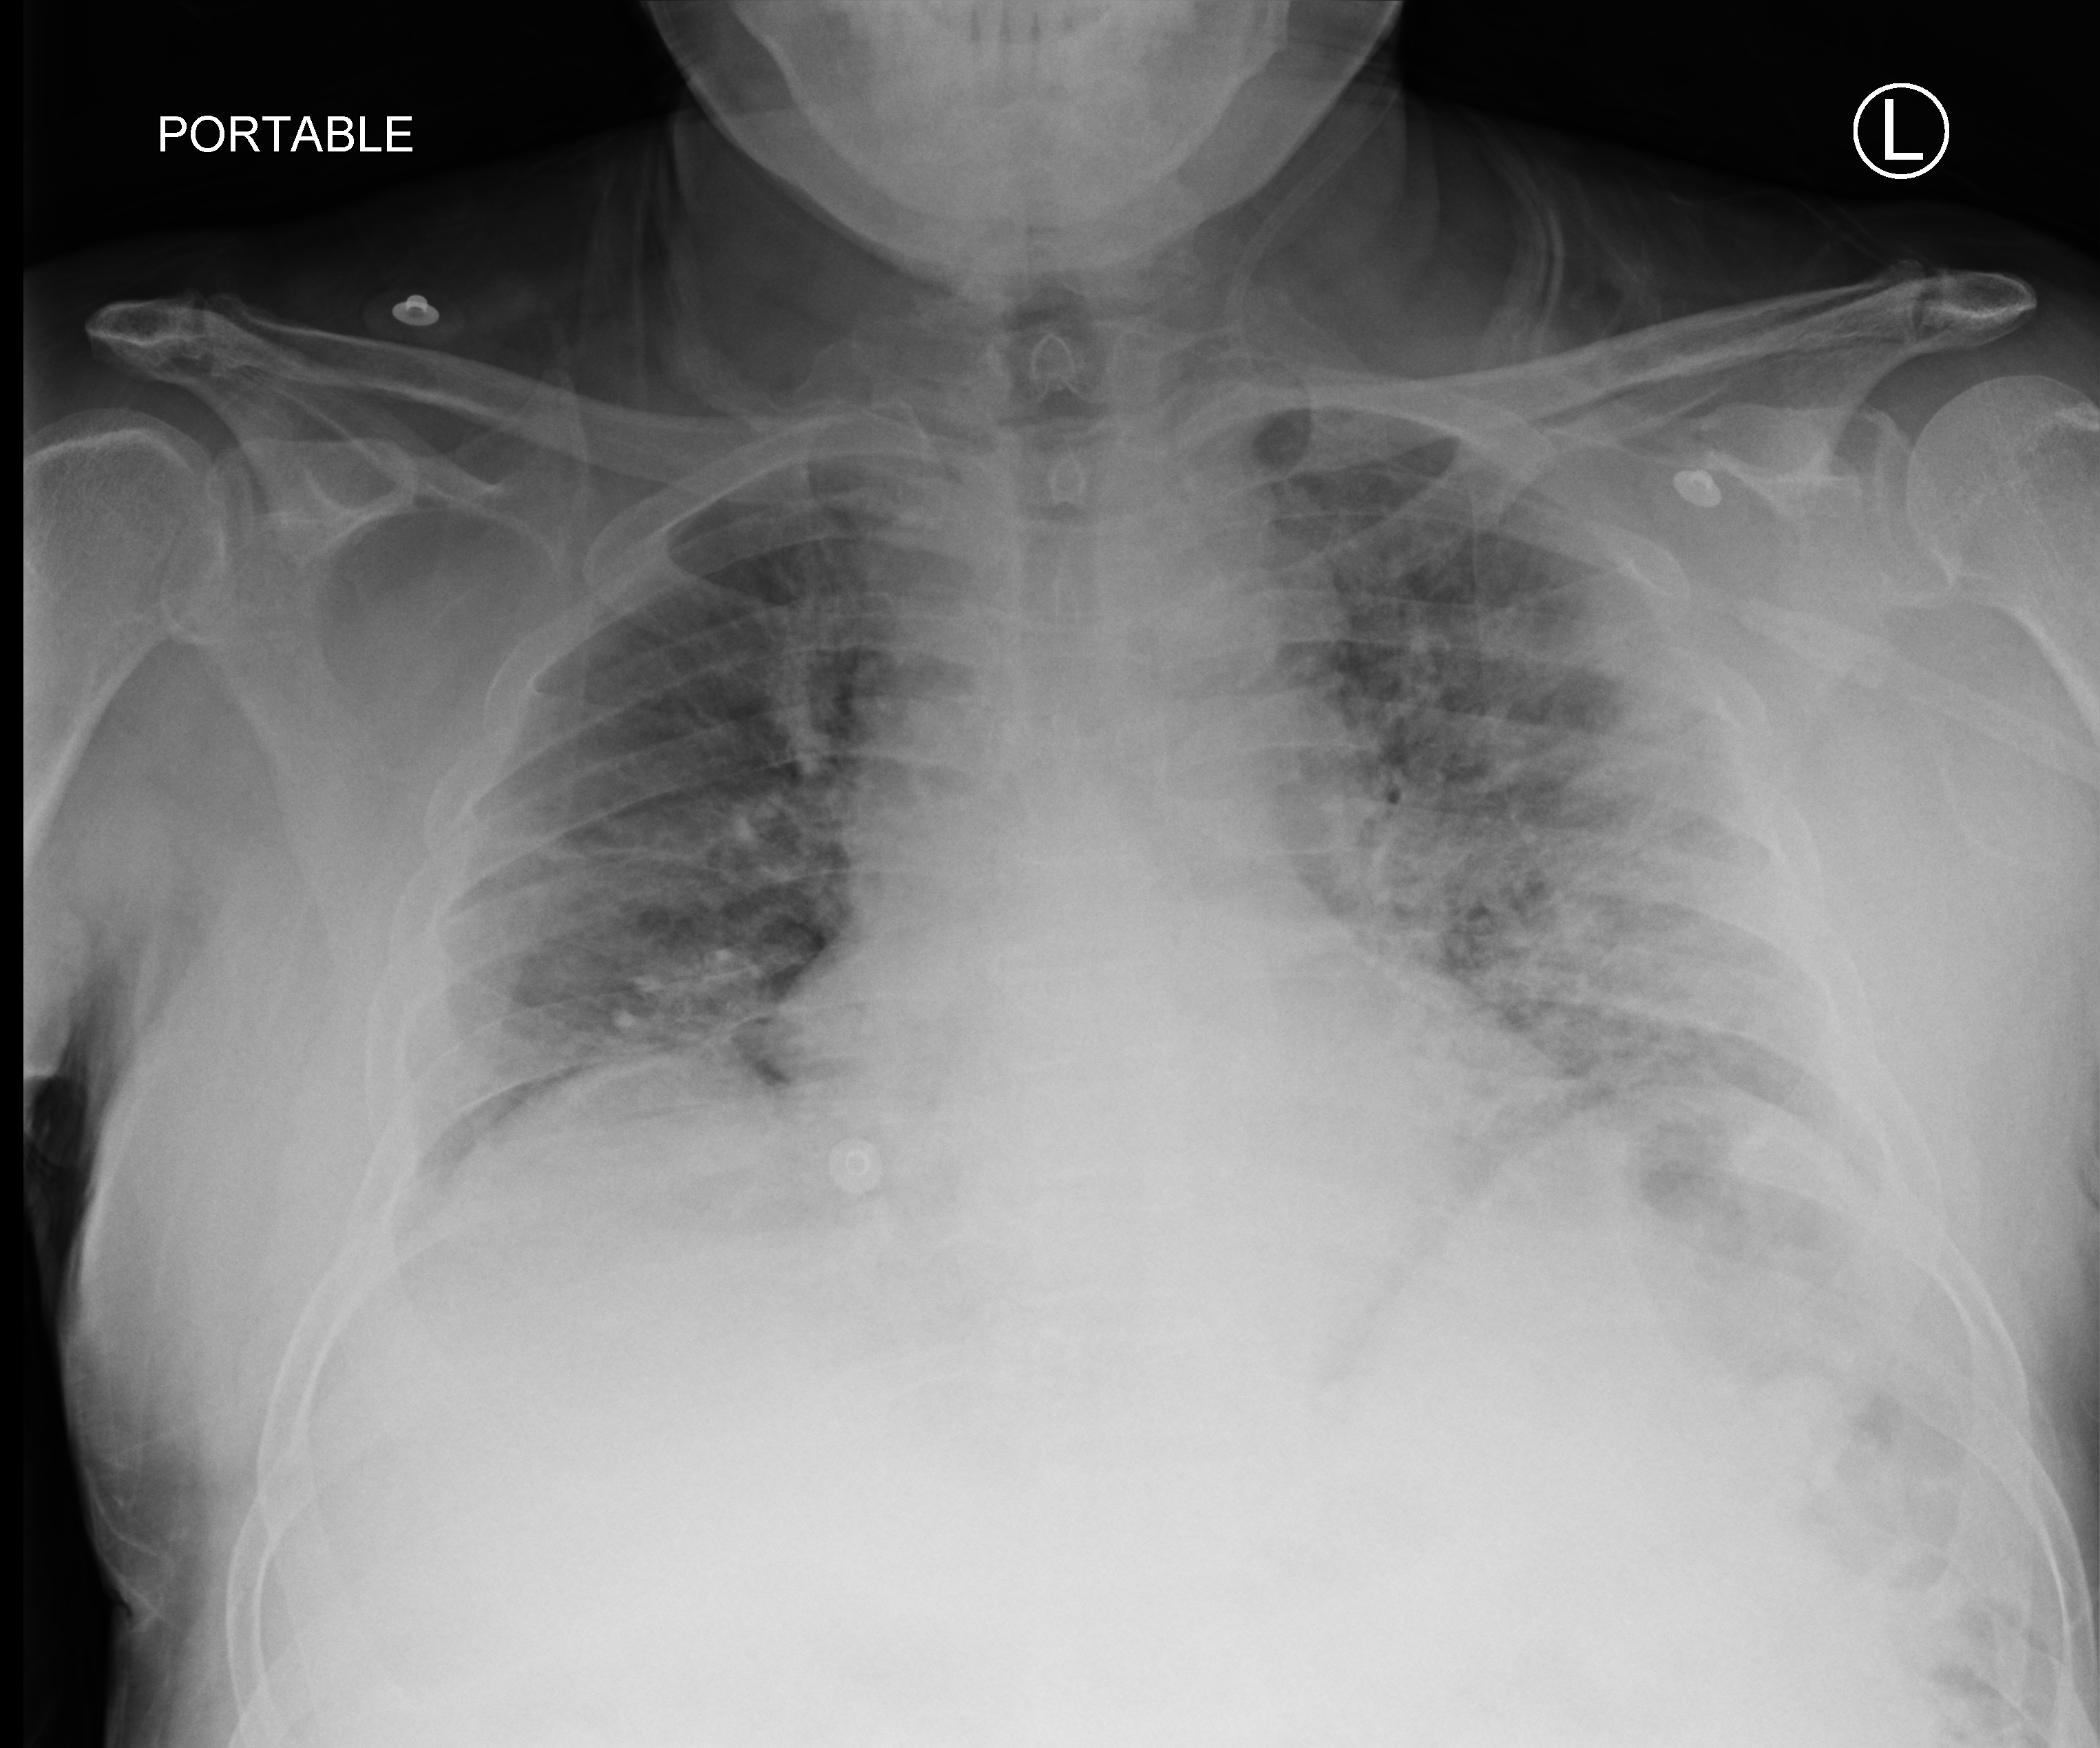
Bedside chest radiograph (computed radiography); anteroposterior (AP) projection. Male patient hospitalised with COVID-19, age 60–74 years.
Admission-level facts for this patient (not findings on this image; timing relative to this image not recorded): mechanically ventilated during this hospital stay: no.